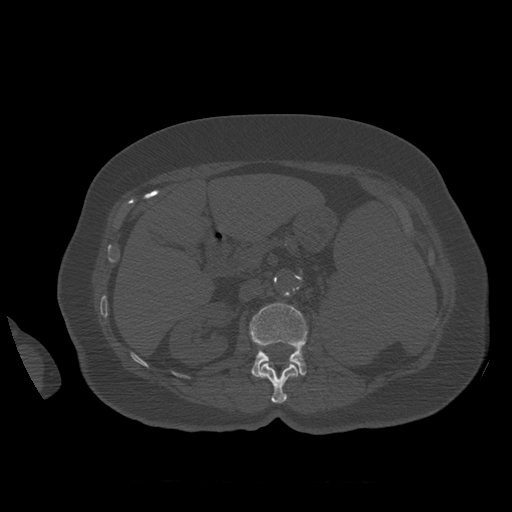
CT including the spine, one axial slice; position 264 of 399 along the scan axis; reconstruction kernel STANDARD; 120 kVp; bone window (W 1800 / L 400 HU); 512 × 512 image matrix. Patient age 81 years. From the clinical record (not read from this slice): primary cancer: renal; vertebrae with lytic lesions (as recorded): L1.
Structures marked on this image (semi-automatically segmented with operator editing):
- L1 vertebra: bounding box [x1, y1, x2, y2] px = [258, 363, 299, 404]
- L2 vertebra: [250, 303, 308, 378]